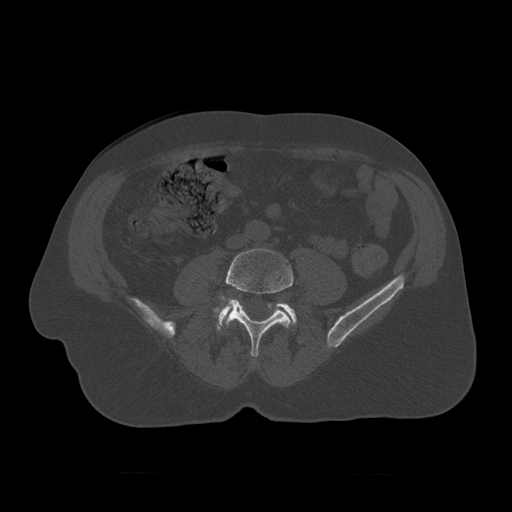
CT including the spine, one axial slice; position 273 of 450 along the scan axis; reconstruction kernel STANDARD; 120 kVp; bone window (W 1800 / L 400 HU); 1.25 mm slice thickness; 512 × 512 image matrix, field of view 405 × 405 mm. Patient age 75 years. Case-level facts recorded for this patient, not image findings: primary cancer: prostate.
Structures marked on this image (semi-automatic segmentation, software-assisted and operator-edited):
- L4 vertebra: box from (x=213, y=249) to (x=294, y=357) px
- L5 vertebra: (x=215, y=302)–(x=297, y=331)